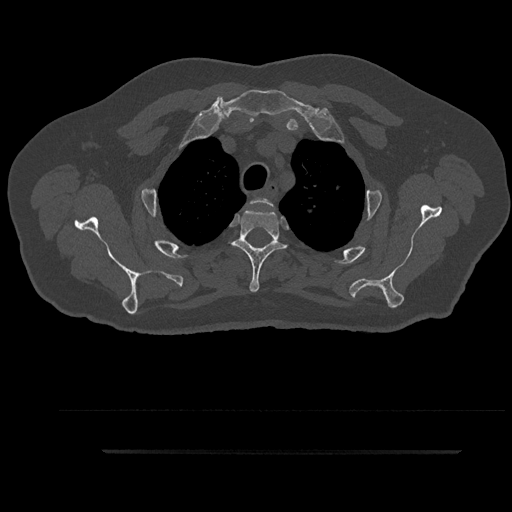
CT including the spine, one axial slice. Slice 716 of 797 in the series (ordered by position). Reconstruction kernel Br40s/3. 120 kVp. Bone window (W 1800 / L 400 HU). 512 × 512 image matrix, field of view 432 × 432 mm. Male patient, age 63 years. From the clinical record (not read from this slice): primary cancer: renal; vertebrae with lytic lesions (as recorded): T8.
Annotated regions visible in this slice (semi-automatic segmentation, software-assisted and operator-edited):
- T2 vertebra: bounding box <251,198,273,207> (left, top, right, bottom; pixels)
- T3 vertebra: <232,209,286,292>